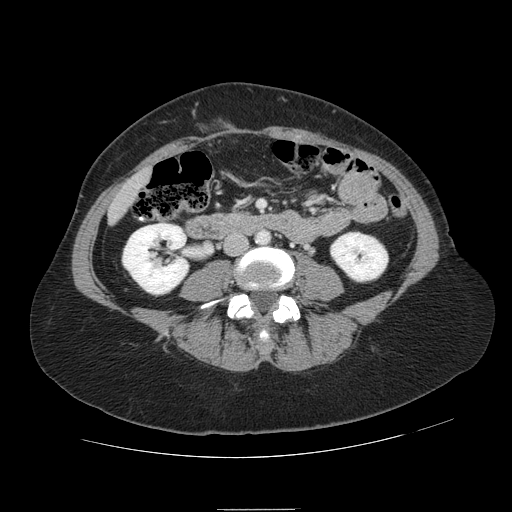
Contrast-enhanced abdominal CT, one axial slice; slice 3 of 121 in the series (ordered by position); intravenous contrast given; soft-tissue window (W 400 / L 40 HU); 2.5 mm slice thickness; 512 × 512 image matrix, field of view 400 × 400 mm. Female patient, age 52 years. Case-level facts recorded for this patient, not image findings: diagnosis: colorectal cancer liver metastases, imaged before liver resection; multiple liver metastases: yes.
Annotated regions visible in this slice (expert manual segmentation):
- liver: bounding box (x1, y1, x2, y2) in pixels: (111, 172, 148, 219)